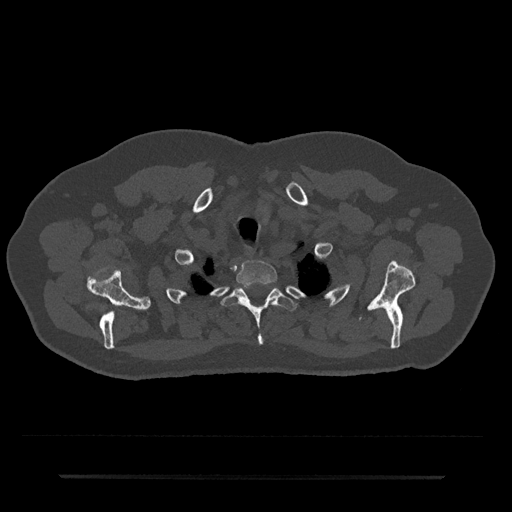
CT including the spine, one axial slice. Slice 617 of 797 in the series (ordered by position). Reconstruction kernel Br40s/3. 120 kVp. Bone window (W 1800 / L 400 HU). 0.5 mm slice thickness. 512 × 512 image matrix, field of view 437 × 437 mm. Patient: male, 69 years. Case-level facts recorded for this patient, not image findings: primary cancer: prostate.
Annotated regions visible in this slice (semi-automatically segmented with operator editing):
- T1 vertebra: box from (x=236, y=260) to (x=278, y=287) px
- T2 vertebra: (x=222, y=285)–(x=296, y=345)